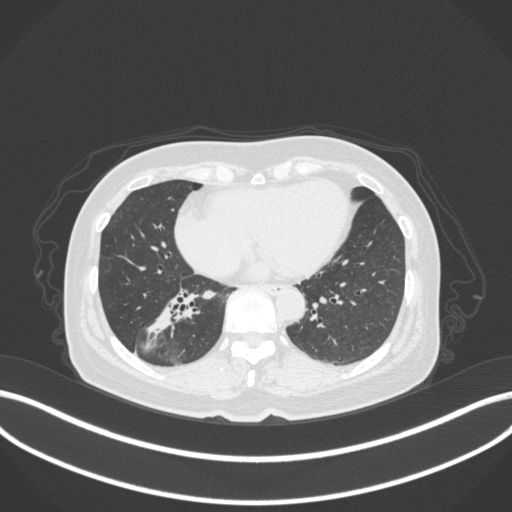
Chest CT, one axial slice. Slice 146 of 429 in the series (ordered by position). 120 kVp. Lung window (W 1500 / L -600 HU). 1 mm slice thickness. 512 × 512 image matrix, field of view 400 × 400 mm. Patient: female, 67 years. From the clinical record (not read from this slice): clinical TNM (as recorded): T1c N1 M0.
Annotated regions visible in this slice (bounding box drawn by a radiologist):
- lung tumour (recorded histology: adenocarcinoma): bounding box <137,289,197,344> (left, top, right, bottom; pixels)